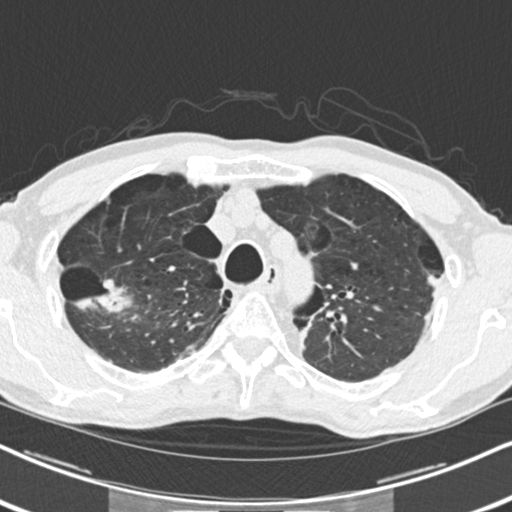
Axial slice from a low-dose chest CT screening exam. Baseline annual screen. Lung window (W 1500 / L -600 HU). 2 mm slice thickness. Standard (soft-tissue) reconstruction kernel (B30f). 512 × 512 image matrix. Male, age 71 years at enrolment.
Expert reader's lesion annotation, bounding box [x1, y1, x2, y2] px = [88, 268, 144, 316]. The screening reader recorded 2 non-calcified nodules or masses ≥4 mm on this exam (right upper lobe, left upper lobe); which of them this box marks is not recorded. Official screen result: positive, change unspecified: nodule(s) >= 4 mm or enlarging nodule(s), mass(es), or other non-specific abnormalities suspicious for lung cancer. Participant outcome: lung cancer diagnosed 454 days after this screen — adenocarcinoma, NOS, right upper lobe, well differentiated (G1), stage IA (AJCC 6th edition), 30 mm at pathology.